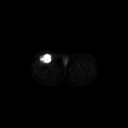
FDG PET of an extremity soft-tissue mass (from a PET/CT study), one axial slice; slice 272 of 311 in the series (ordered by position); 3.27 mm slice thickness; 128 × 128 image matrix. Patient: male, 56 years. Case-level facts recorded for this patient, not image findings: histological type: pleiomorphic leiomyosarcoma; grade: intermediate; site of the primary tumour: right thigh.
Outlined on this slice (expert contour drawn on MRI and transferred to this co-registered scan by the dataset authors):
- gross tumour volume including surrounding oedema: bounding box <39,54,52,64> (left, top, right, bottom; pixels)
- gross tumour volume (mass): <39,54,52,64>